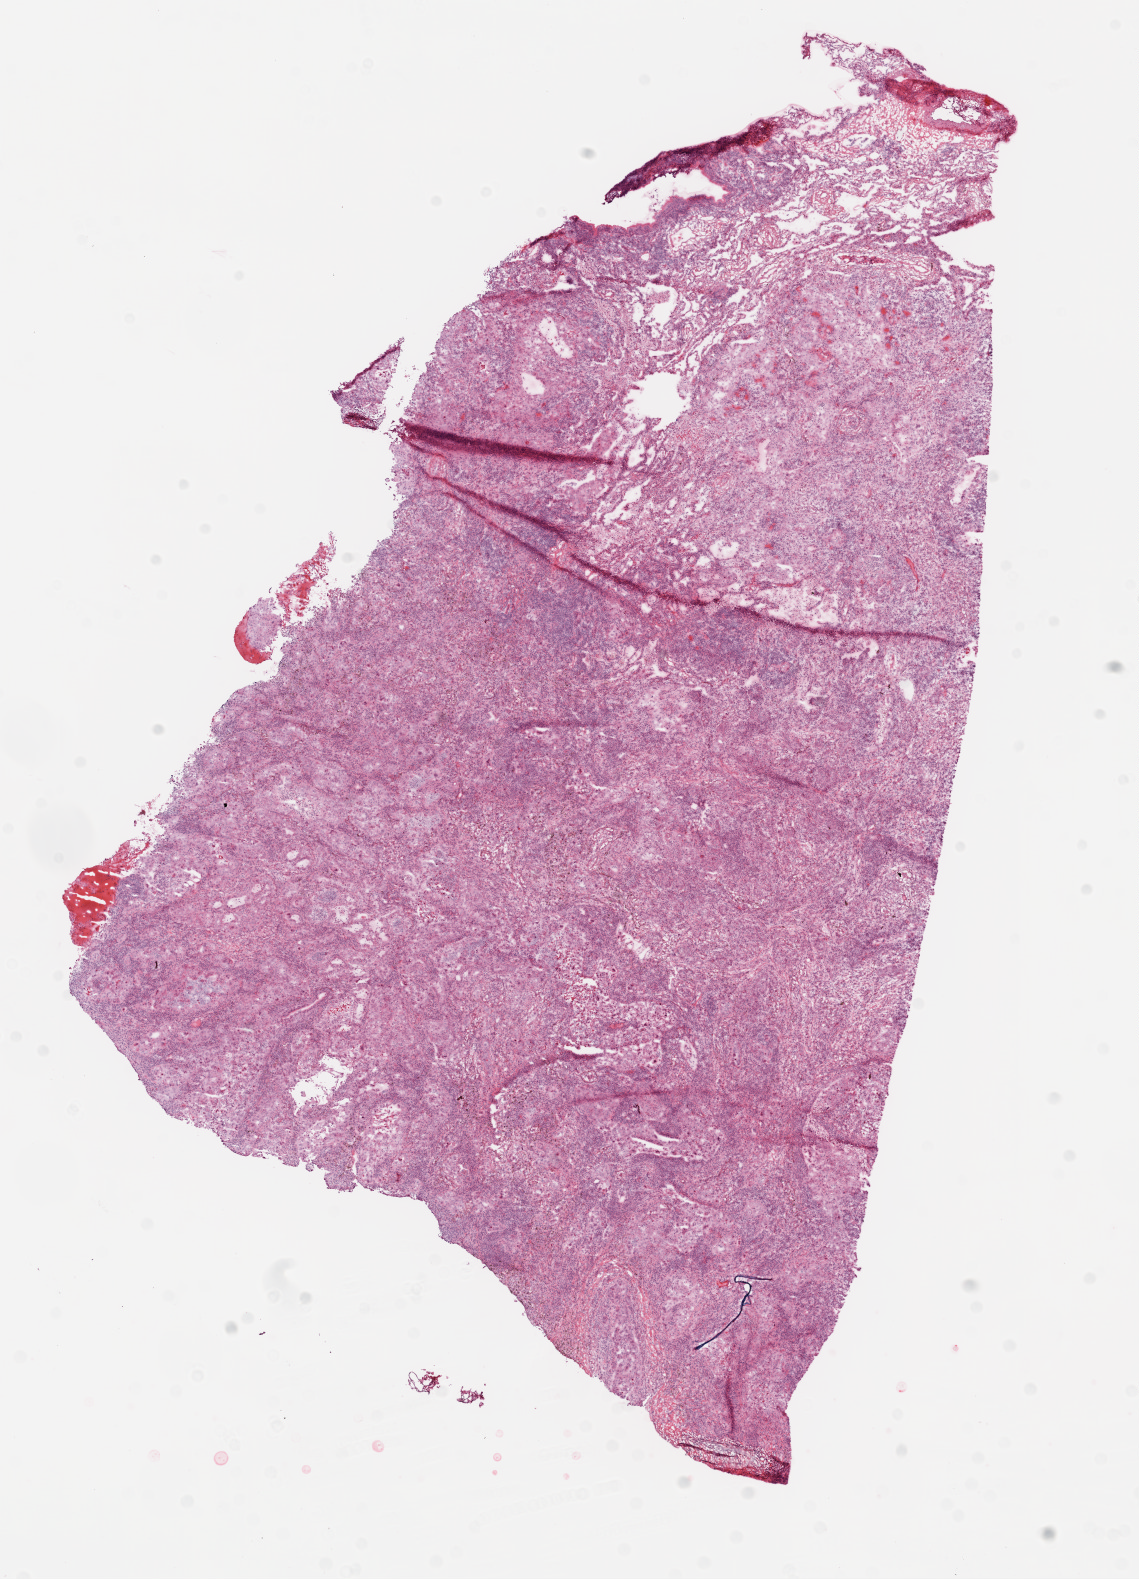
H&E whole-slide image, shown as a low-resolution overview of the whole scanned area (about 9.2 x 12.7 mm, from a 20x scan). Frozen section. Primary tumour sample from the lung. Patient: male, age at initial diagnosis 63 years. Pathologist review of this section (percent, as recorded): tumour nuclei 75%, necrosis 0%.
Diagnosis: Squamous cell carcinoma, NOS. Laterality: right. AJCC pathologic stage: IA.